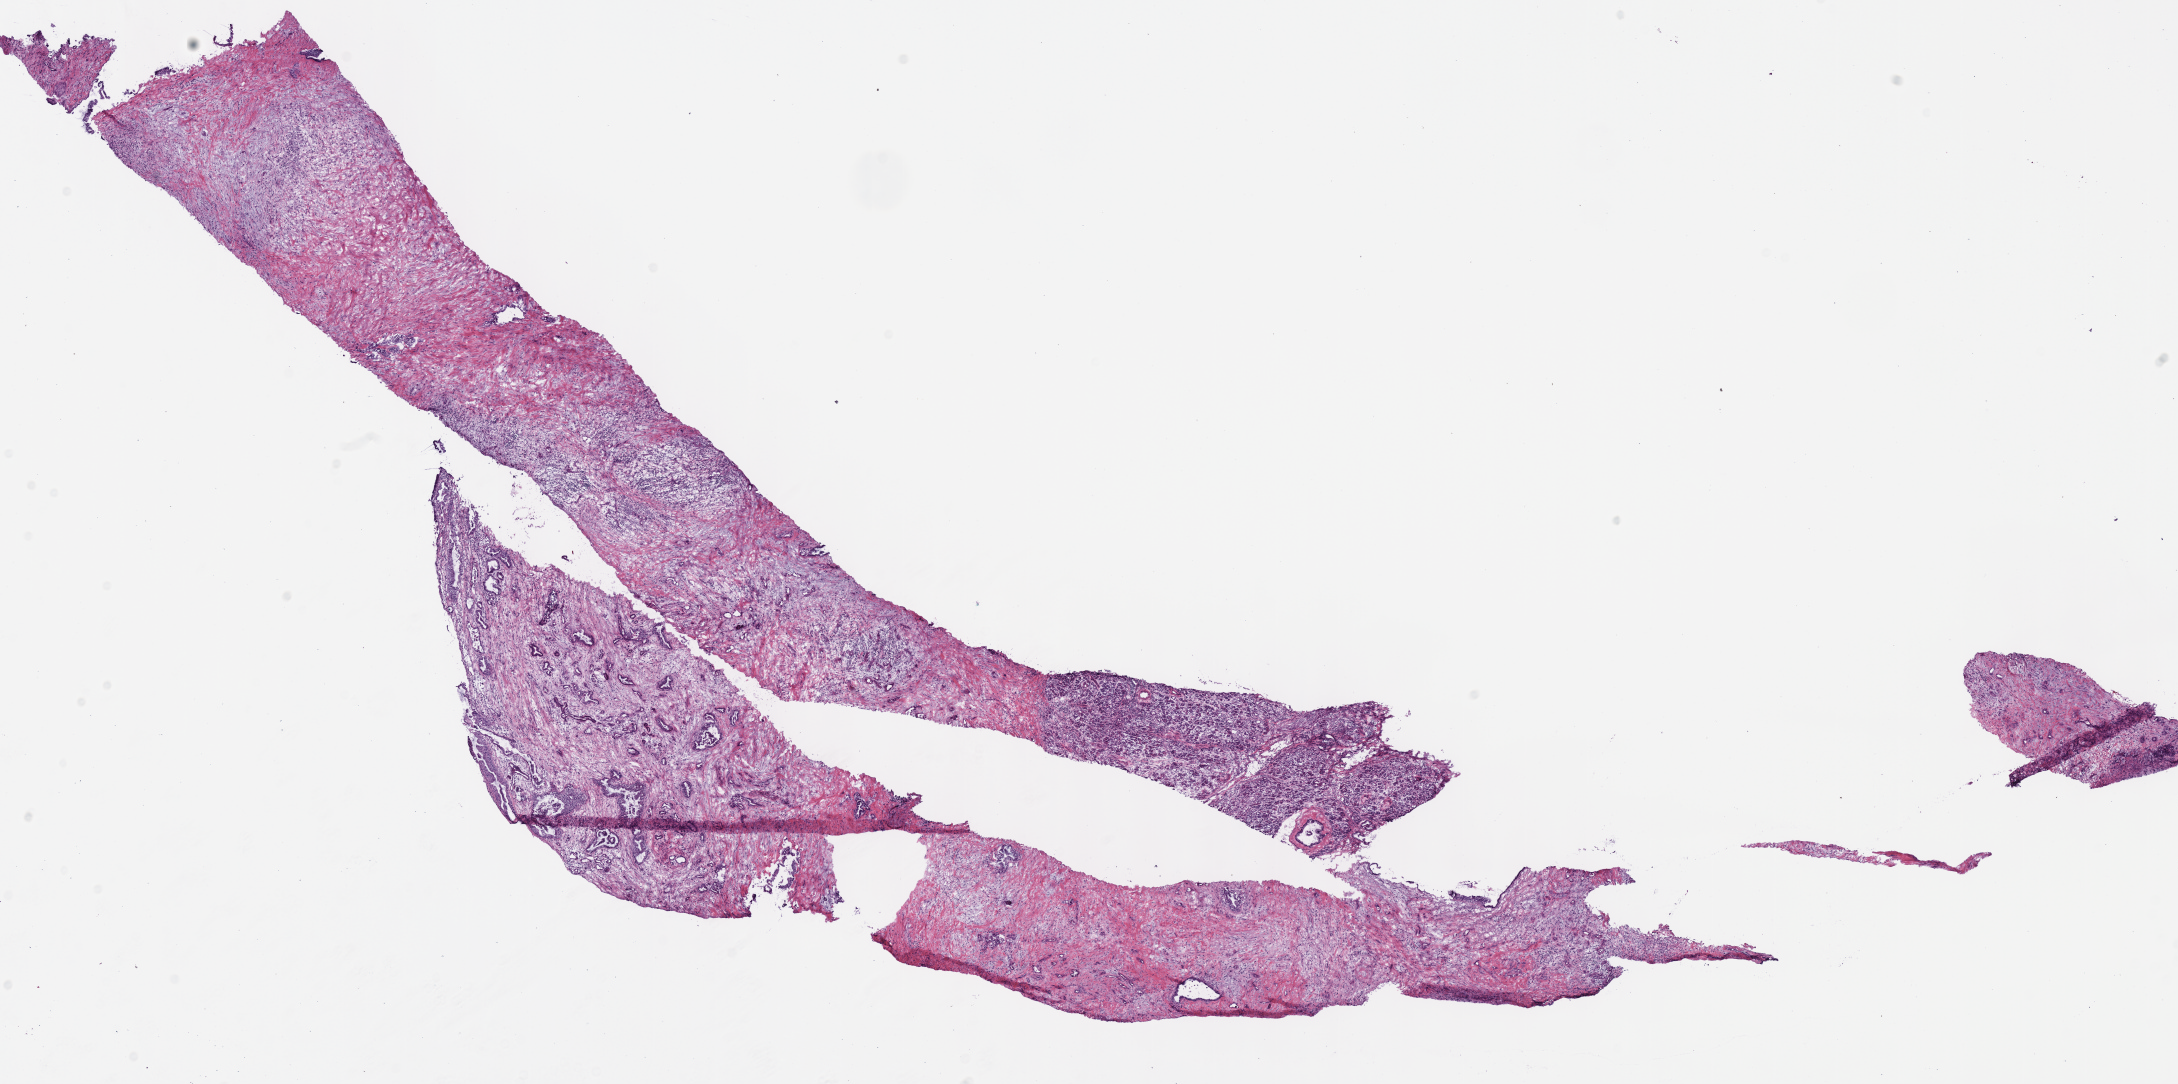
H&E-stained whole-slide image — whole scanned area (about 17.1 x 8.5 mm, acquisition: 40x scan) shown as a low-resolution overview; frozen section from the bottom of the tissue portion; pancreas, primary tumour sample. Patient: female, age at initial diagnosis 85 years.
Diagnosis: Infiltrating duct carcinoma, NOS.